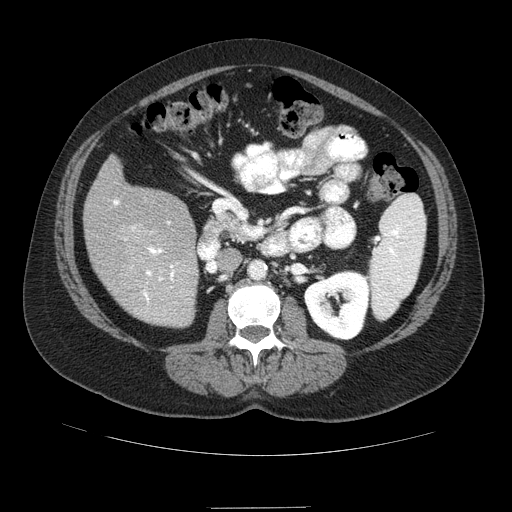
Contrast-enhanced abdominal CT (liver protocol), one axial slice. Position 32 of 89 along the scan axis. Reconstruction kernel STANDARD. Soft-tissue window (W 400 / L 40 HU). 2.5 mm slice thickness. 512 × 512 image matrix, field of view 400 × 400 mm. From the clinical record (not read from this slice): diagnosis: hepatocellular carcinoma (patient treated with transarterial chemoembolisation; whether this scan precedes or follows treatment is not stated here); TNM stage (as recorded): Stage-IIIB; Child-Pugh class: A.
Structures marked on this image (semi-automatically segmented with operator editing):
- liver parenchyma outside the tumour (the mass and vessels are separate outlines, so this box may not span the whole liver): bounding box (x1, y1, x2, y2) in pixels: (84, 156, 198, 326)
- liver vessels: (113, 199, 175, 302)